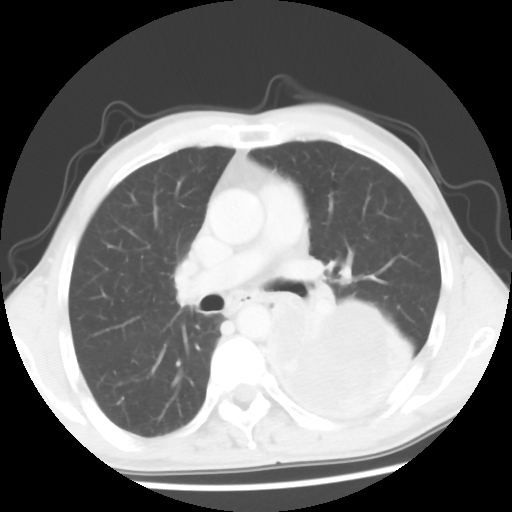
Chest CT, one axial slice. Slice 33 of 56 in the series (ordered by position). Reconstruction kernel STANDARD. 120 kVp. Lung window (W 1500 / L -600 HU). 5 mm slice thickness. 512 × 512 image matrix, field of view 318 × 318 mm. Patient: male, 60 years. From the clinical record (not read from this slice): clinical TNM (as recorded): T4 N0 M0.
Structures marked on this image (bounding box drawn by a radiologist):
- lung tumour (recorded histology: squamous cell carcinoma): bounding box [x1, y1, x2, y2] px = [254, 293, 425, 432]